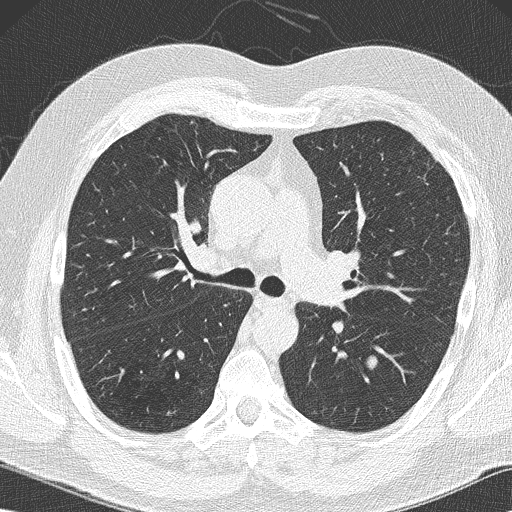
Chest CT (low-dose screening protocol), one axial image; baseline screening round; lung window (W 1500 / L -600 HU); 2 mm slice thickness; lung (sharp) reconstruction kernel (B50f); 120 kVp. Male participant, aged 59 years at enrolment. Former smoker at enrolment.
Expert reader's lesion annotation, bounding box (x1, y1, x2, y2) in pixels: (344, 345, 389, 384). The screening reader recorded 2 non-calcified nodules or masses ≥4 mm on this exam; which of them this box marks is not recorded. Participant outcome: lung cancer diagnosed 61 days after this screen — large cell carcinoma, NOS, left lower lobe, poorly differentiated (G3), stage IA (AJCC 6th edition), 14 mm at pathology.